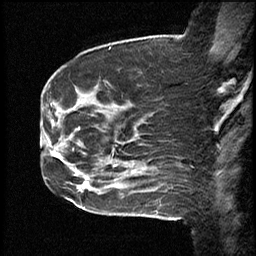
Breast MRI (dynamic contrast-enhanced), one sagittal slice; dynamic contrast-enhanced study with each time point stored as its own series, time point 2 of 4 at this slice position (early post-contrast, ordered by acquisition time); 1.5 T; TE 4.2 ms, TR 18.3 ms; 3 mm slice thickness; 256 × 256 image matrix, field of view 200 × 200 mm. From the clinical record (not read from this slice): setting: breast cancer imaged before/during neoadjuvant chemotherapy; receptor status: HR-positive, HER2-negative.
Structures marked on this image (semi-automatic segmentation, software-assisted and operator-edited):
- analysis volume of interest (the breast-tissue region the enhancement analysis was run in; not a lesion): bounding box <64,82,111,209> (left, top, right, bottom; pixels)
- tumour enhancement mask (voxels above the 100 % enhancement threshold inside the analysis volume of interest): <86,177,89,184>